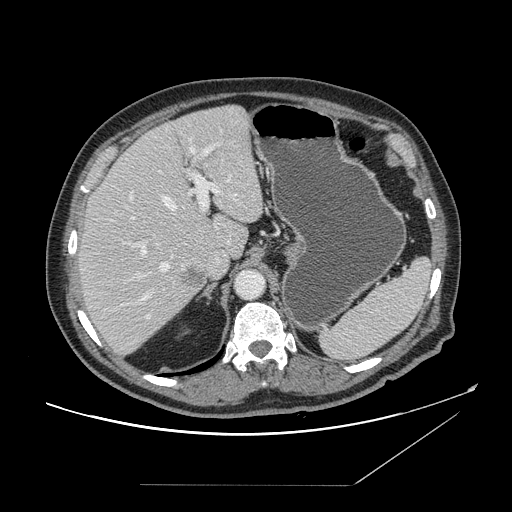
Contrast-enhanced abdominal CT, one axial slice; position 109 of 166 along the scan axis; 120 kVp; soft-tissue window (W 400 / L 40 HU); 2.5 mm slice thickness; 512 × 512 image matrix. Male patient, age 80 years. Case-level facts recorded for this patient, not image findings: diagnosis: colorectal cancer liver metastases, imaged before liver resection; multiple liver metastases: no; largest metastasis: 2.2 cm; chemotherapy before resection: no.
Structures marked on this image (expert manual segmentation):
- hepatic veins: bounding box <132,140,196,304> (left, top, right, bottom; pixels)
- liver: <78,106,263,356>
- planned liver remnant (the part of the liver to remain after resection): <86,106,263,258>
- portal vein (with intrahepatic branches): <130,145,230,318>
- liver metastasis: <185,270,205,290>
- liver metastasis: <181,268,206,288>